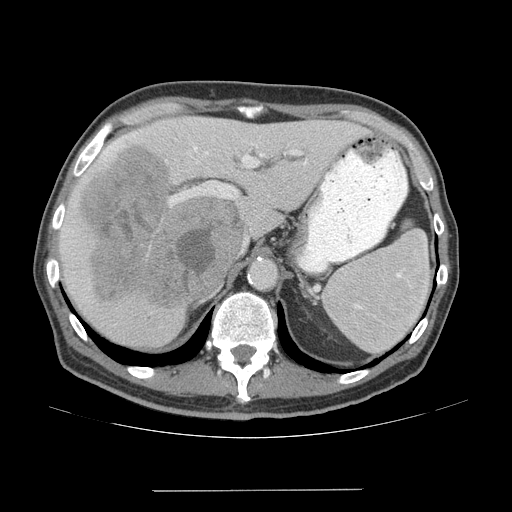
Contrast-enhanced abdominal CT (liver protocol), one axial slice. Position 43 of 77 along the scan axis. Reconstruction kernel STANDARD. 140 kVp. Soft-tissue window (W 400 / L 40 HU). 2.5 mm slice thickness. 512 × 512 image matrix. Case-level facts recorded for this patient, not image findings: diagnosis: hepatocellular carcinoma (patient treated with transarterial chemoembolisation; whether this scan precedes or follows treatment is not stated here); TNM stage (as recorded): Stage-IVA; Child-Pugh class: A.
Annotated regions visible in this slice (semi-automatically segmented with operator editing):
- liver parenchyma outside the tumour (the mass and vessels are separate outlines, so this box may not span the whole liver): bounding box <58,116,368,346> (left, top, right, bottom; pixels)
- mass: <80,145,249,306>
- liver vessels: <101,132,307,206>